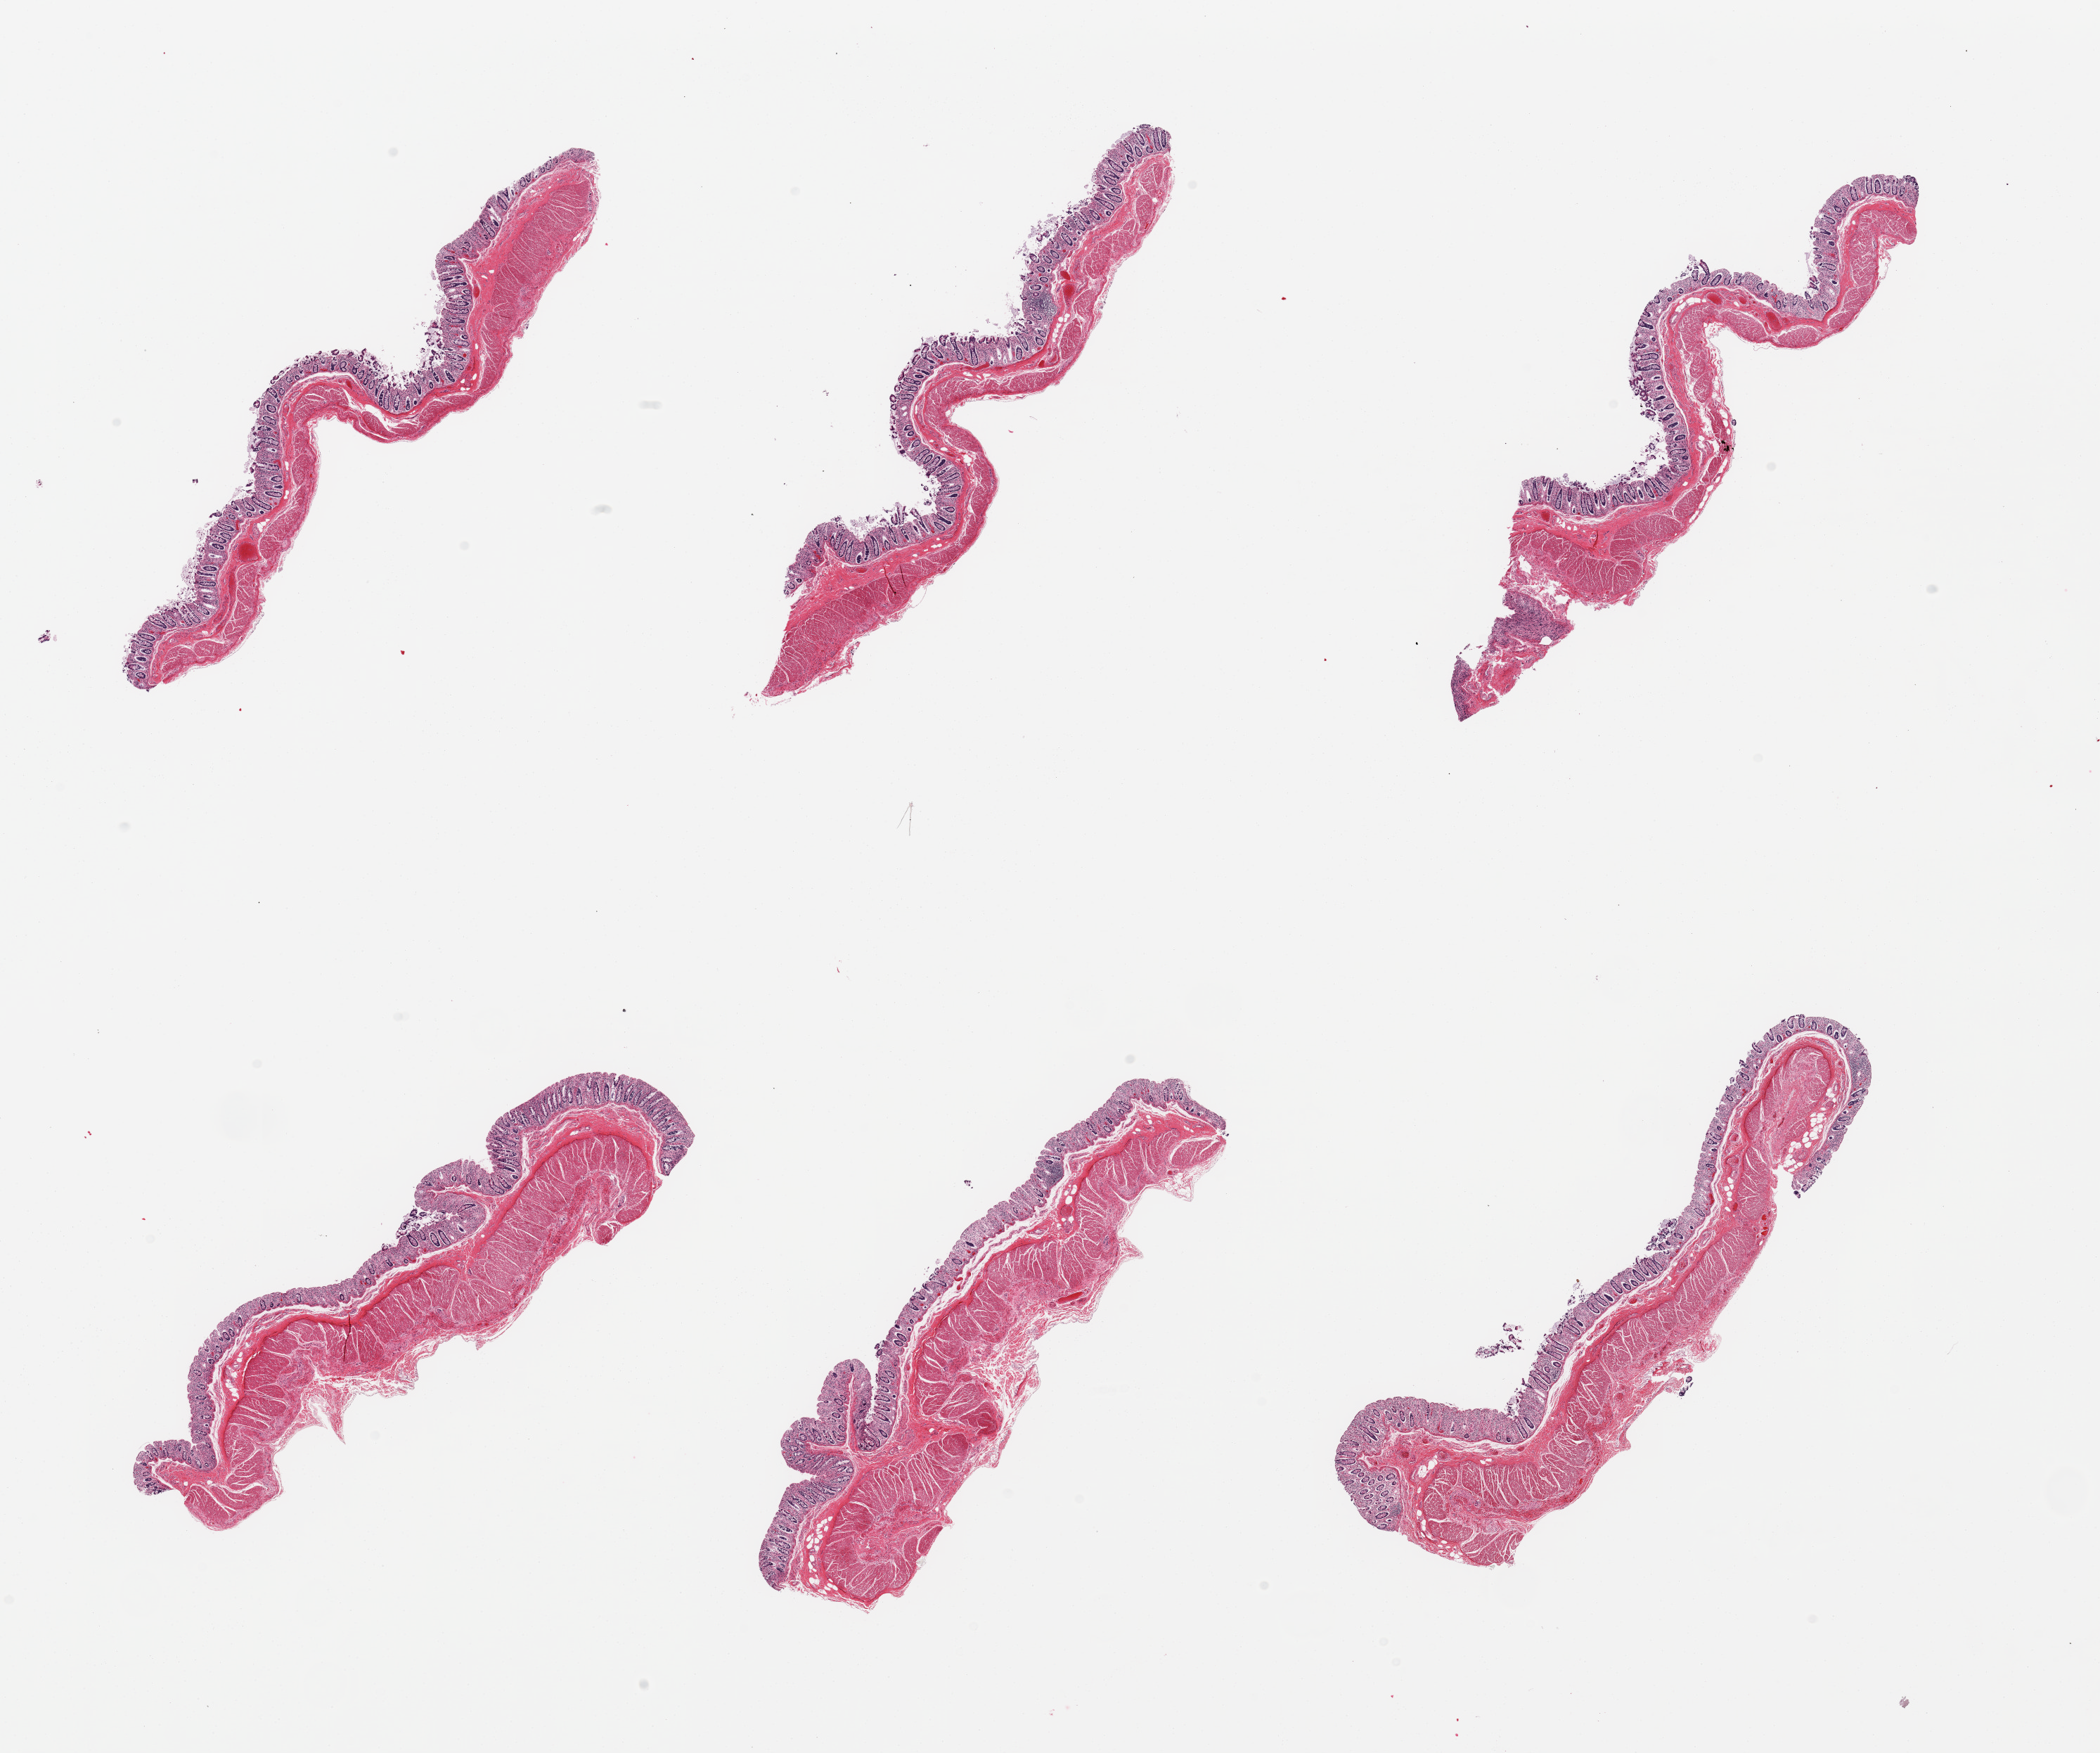
Digitized hematoxylin and eosin (H&E)-stained section, low-resolution overview of the scanned area, about 23.6 x 19.7 mm (slide scanned at 20x), PAXgene-fixed, paraffin-embedded tissue, section of transverse colon (target tissue), tissue donor sample. Donor sex: male.
Reviewer comment on this tissue sample: 6 pieces, muscosa ~30-40% thickness, badly autolyzed.